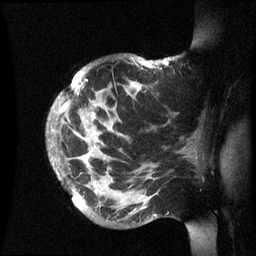
Breast MRI (dynamic contrast-enhanced), one sagittal slice. Slice 46 of 60 in the series (ordered by position). Dynamic contrast-enhanced series, image 2 of 3 at this slice position (ordered by acquisition). 1.5 T. TE 4.2 ms, TR 8.4 ms. 256 × 256 image matrix, field of view 230 × 230 mm. Patient: female, 48 years.
Structures marked on this image (semi-automatically segmented with operator editing):
- analysis volume of interest (the breast-tissue region the enhancement analysis was run in; not a lesion): bounding box <48,57,202,236> (left, top, right, bottom; pixels)
- tumour enhancement mask (voxels above the 70 % enhancement threshold inside the analysis volume of interest): <60,60,167,151>